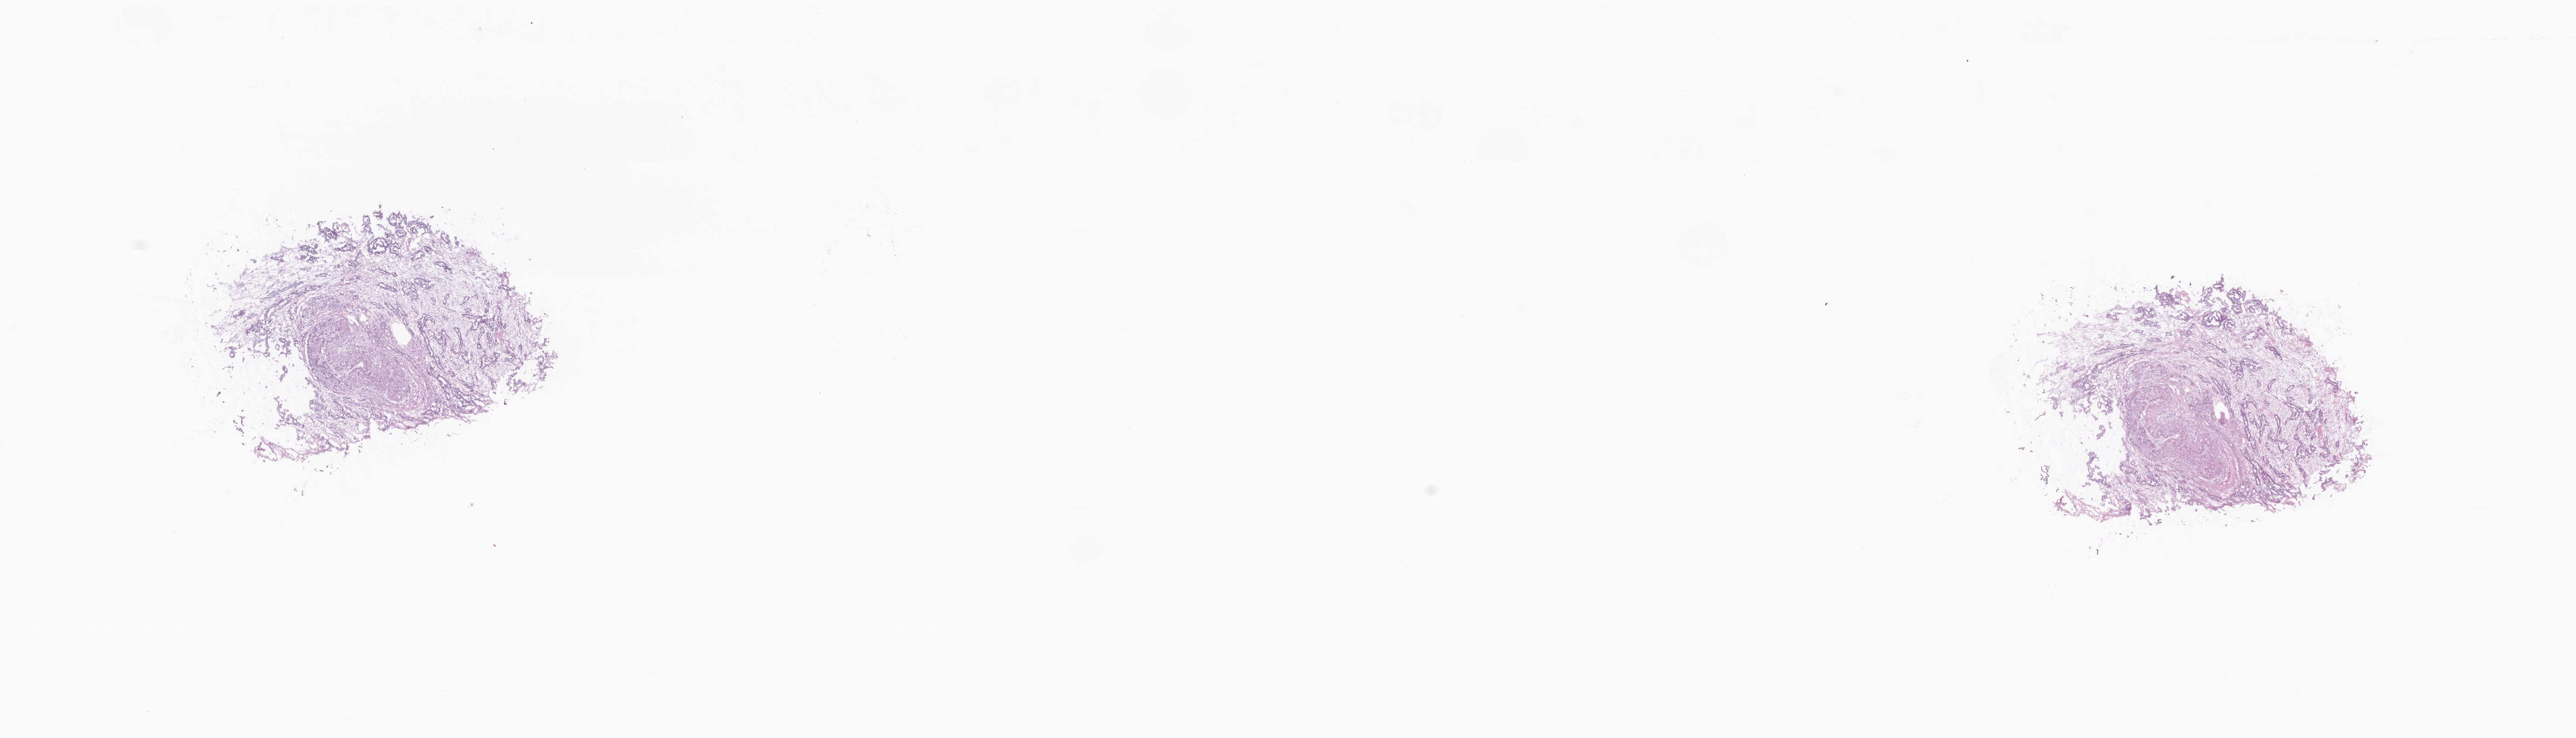
Digitized hematoxylin and eosin (H&E)-stained section — shown as a low-resolution overview of the whole scanned area (about 23.6 x 6.8 mm). Frozen section. Specimen: metastatic tumor tissue. Female patient; age at initial diagnosis 60 years. Pathologist review of this section (percent, as recorded): tumor cells 80%, tumor nuclei 80%, stromal cells 20%, necrosis 0%, normal cells 0%. Infiltration values recorded for this section: lymphocyte infiltration 4%, monocyte infiltration 1%, neutrophil infiltration 5%.
Section: bottom of the tissue portion. Patient diagnosis (primary): Infiltrating duct carcinoma, NOS.